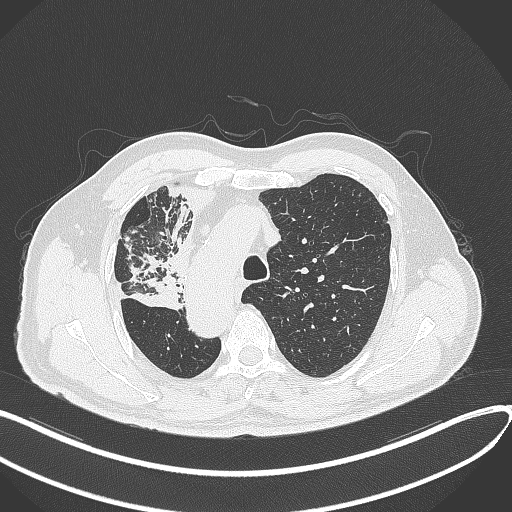
Chest CT, one axial slice. Slice 238 of 300 in the series (ordered by position). Reconstruction kernel B70f. Lung window (W 1500 / L -600 HU). 1 mm slice thickness. 512 × 512 image matrix, field of view 400 × 400 mm. Patient: male, 67 years. From the clinical record (not read from this slice): clinical TNM (as recorded): T2a N0 M0.
Outlined on this slice (rectangle marked by the reading radiologist):
- lung tumour (recorded histology: squamous cell carcinoma): bounding box (x1, y1, x2, y2) in pixels: (128, 245, 183, 315)